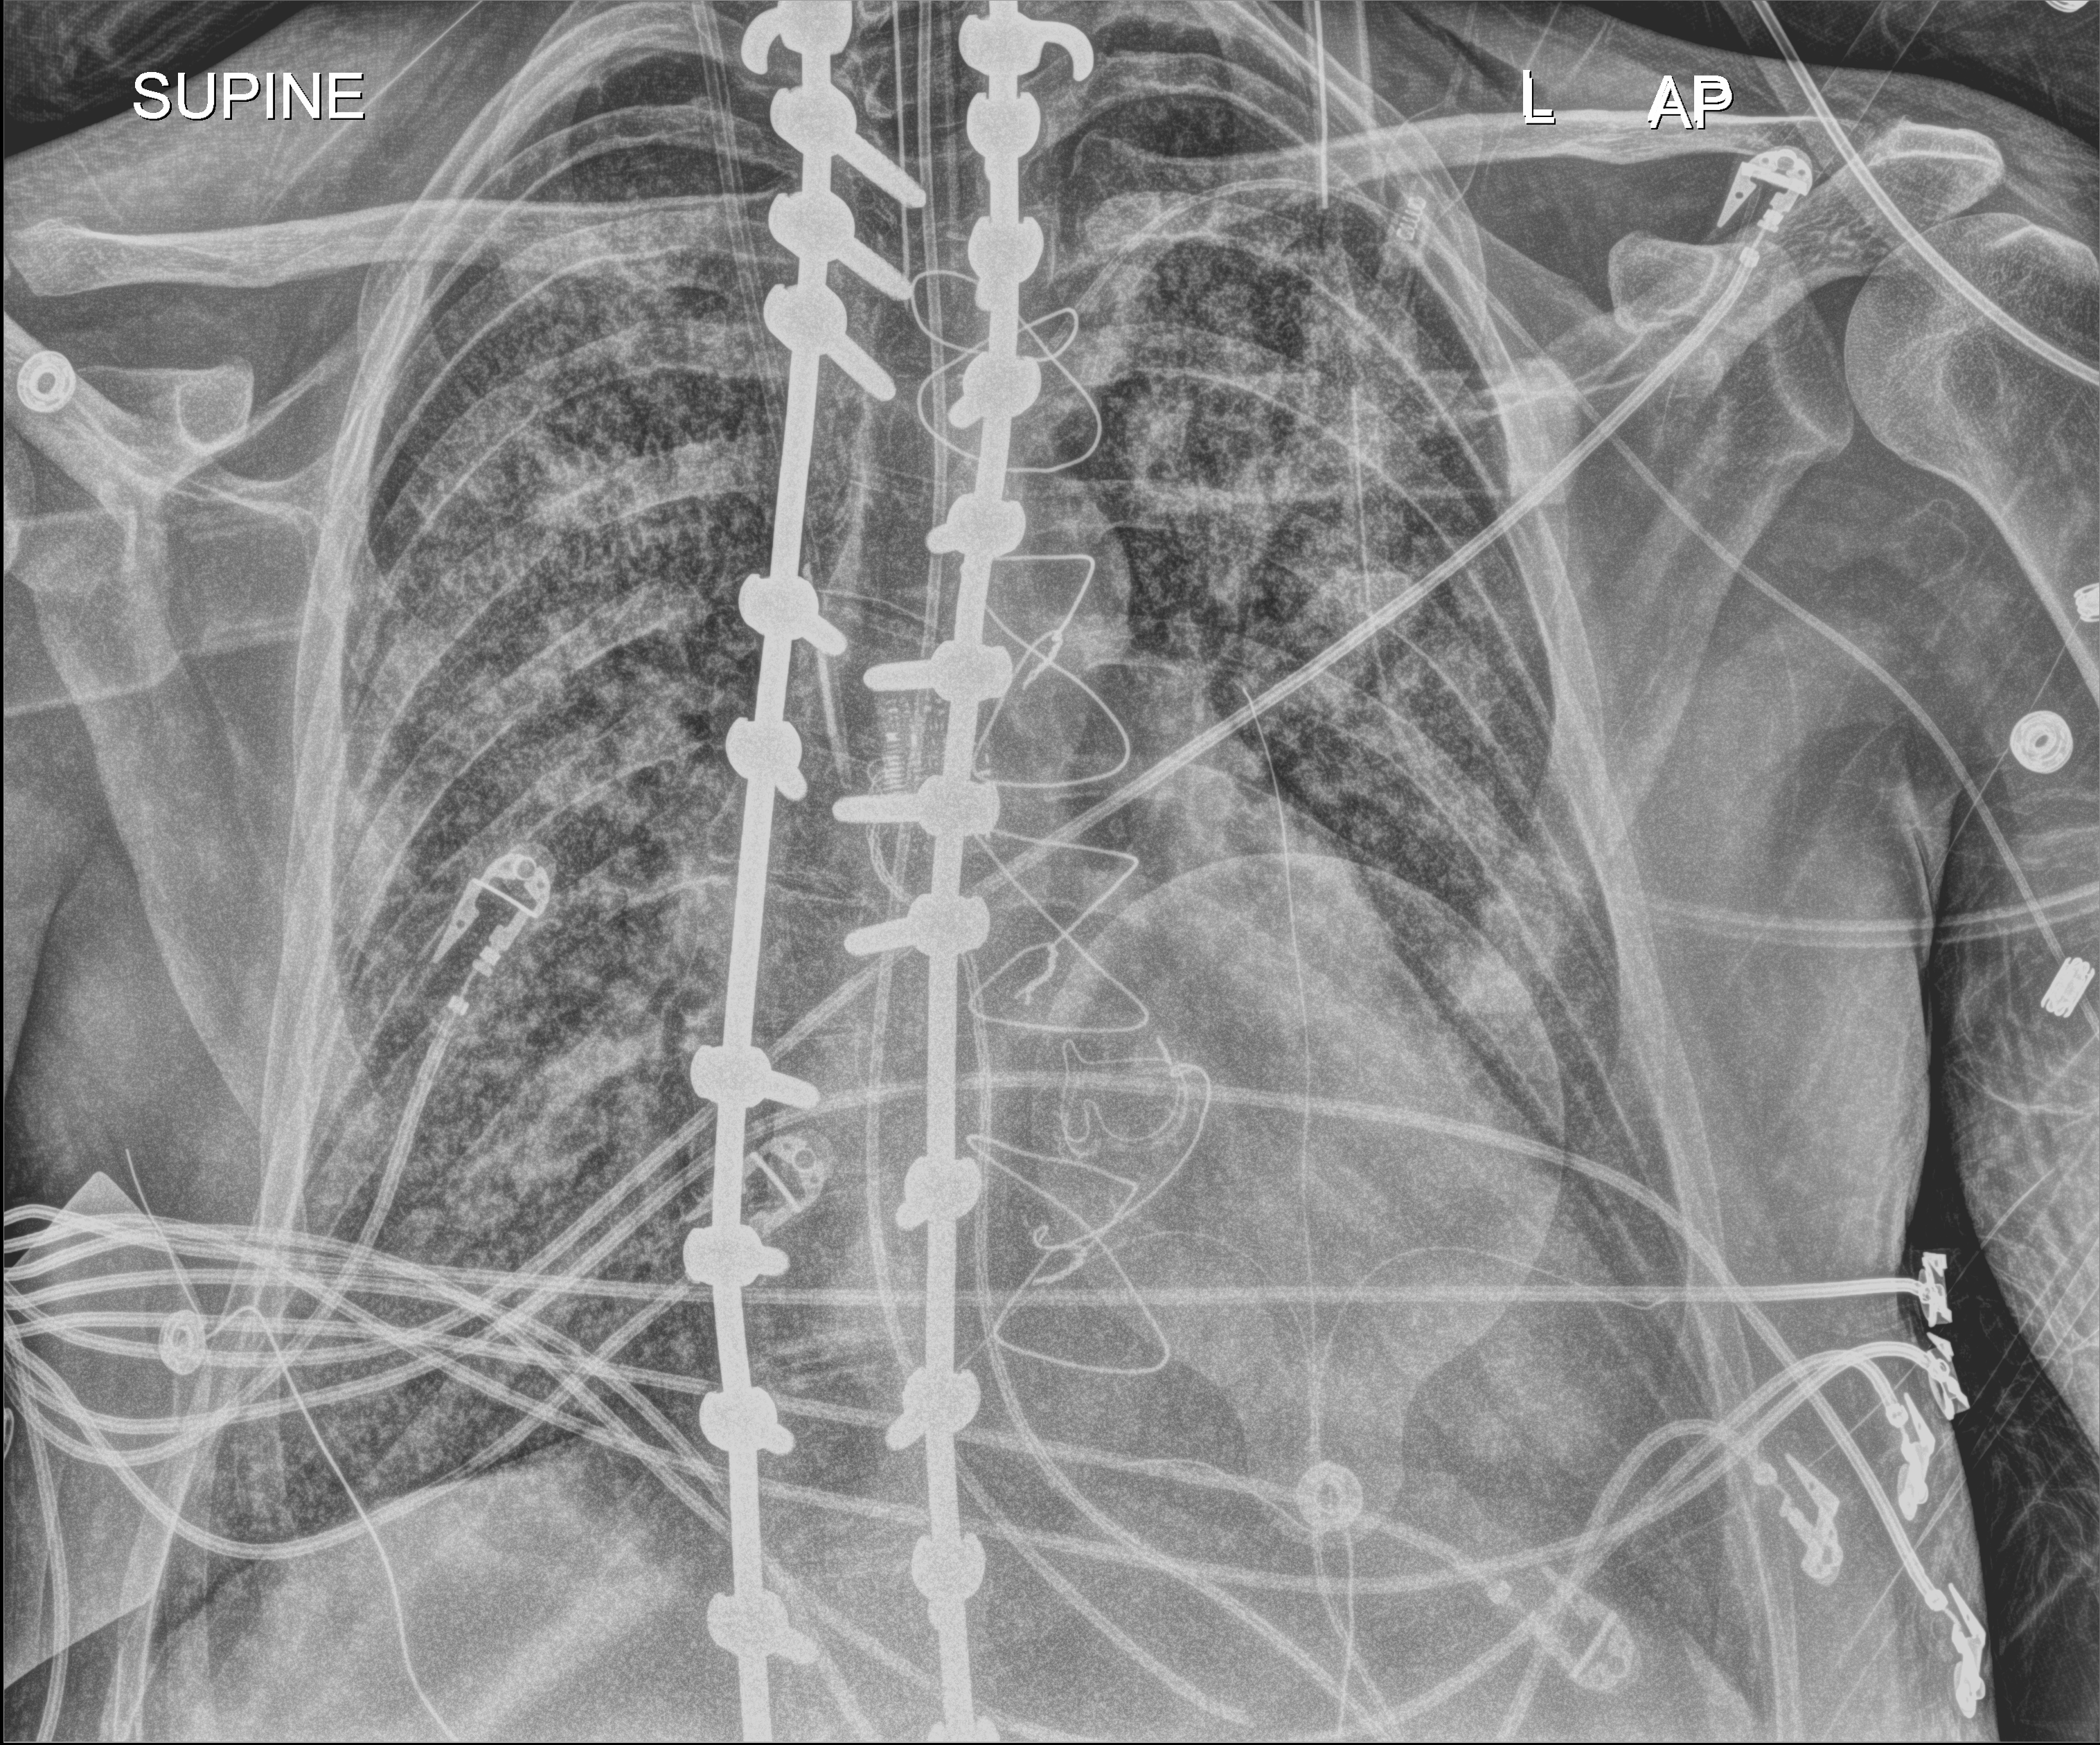
Portable chest radiograph. Adult patient hospitalised with COVID-19, age 18–59 years.
From the hospital-stay record, not from the radiograph (when in the stay this image was taken is not recorded):
- length of hospital stay: 15 days